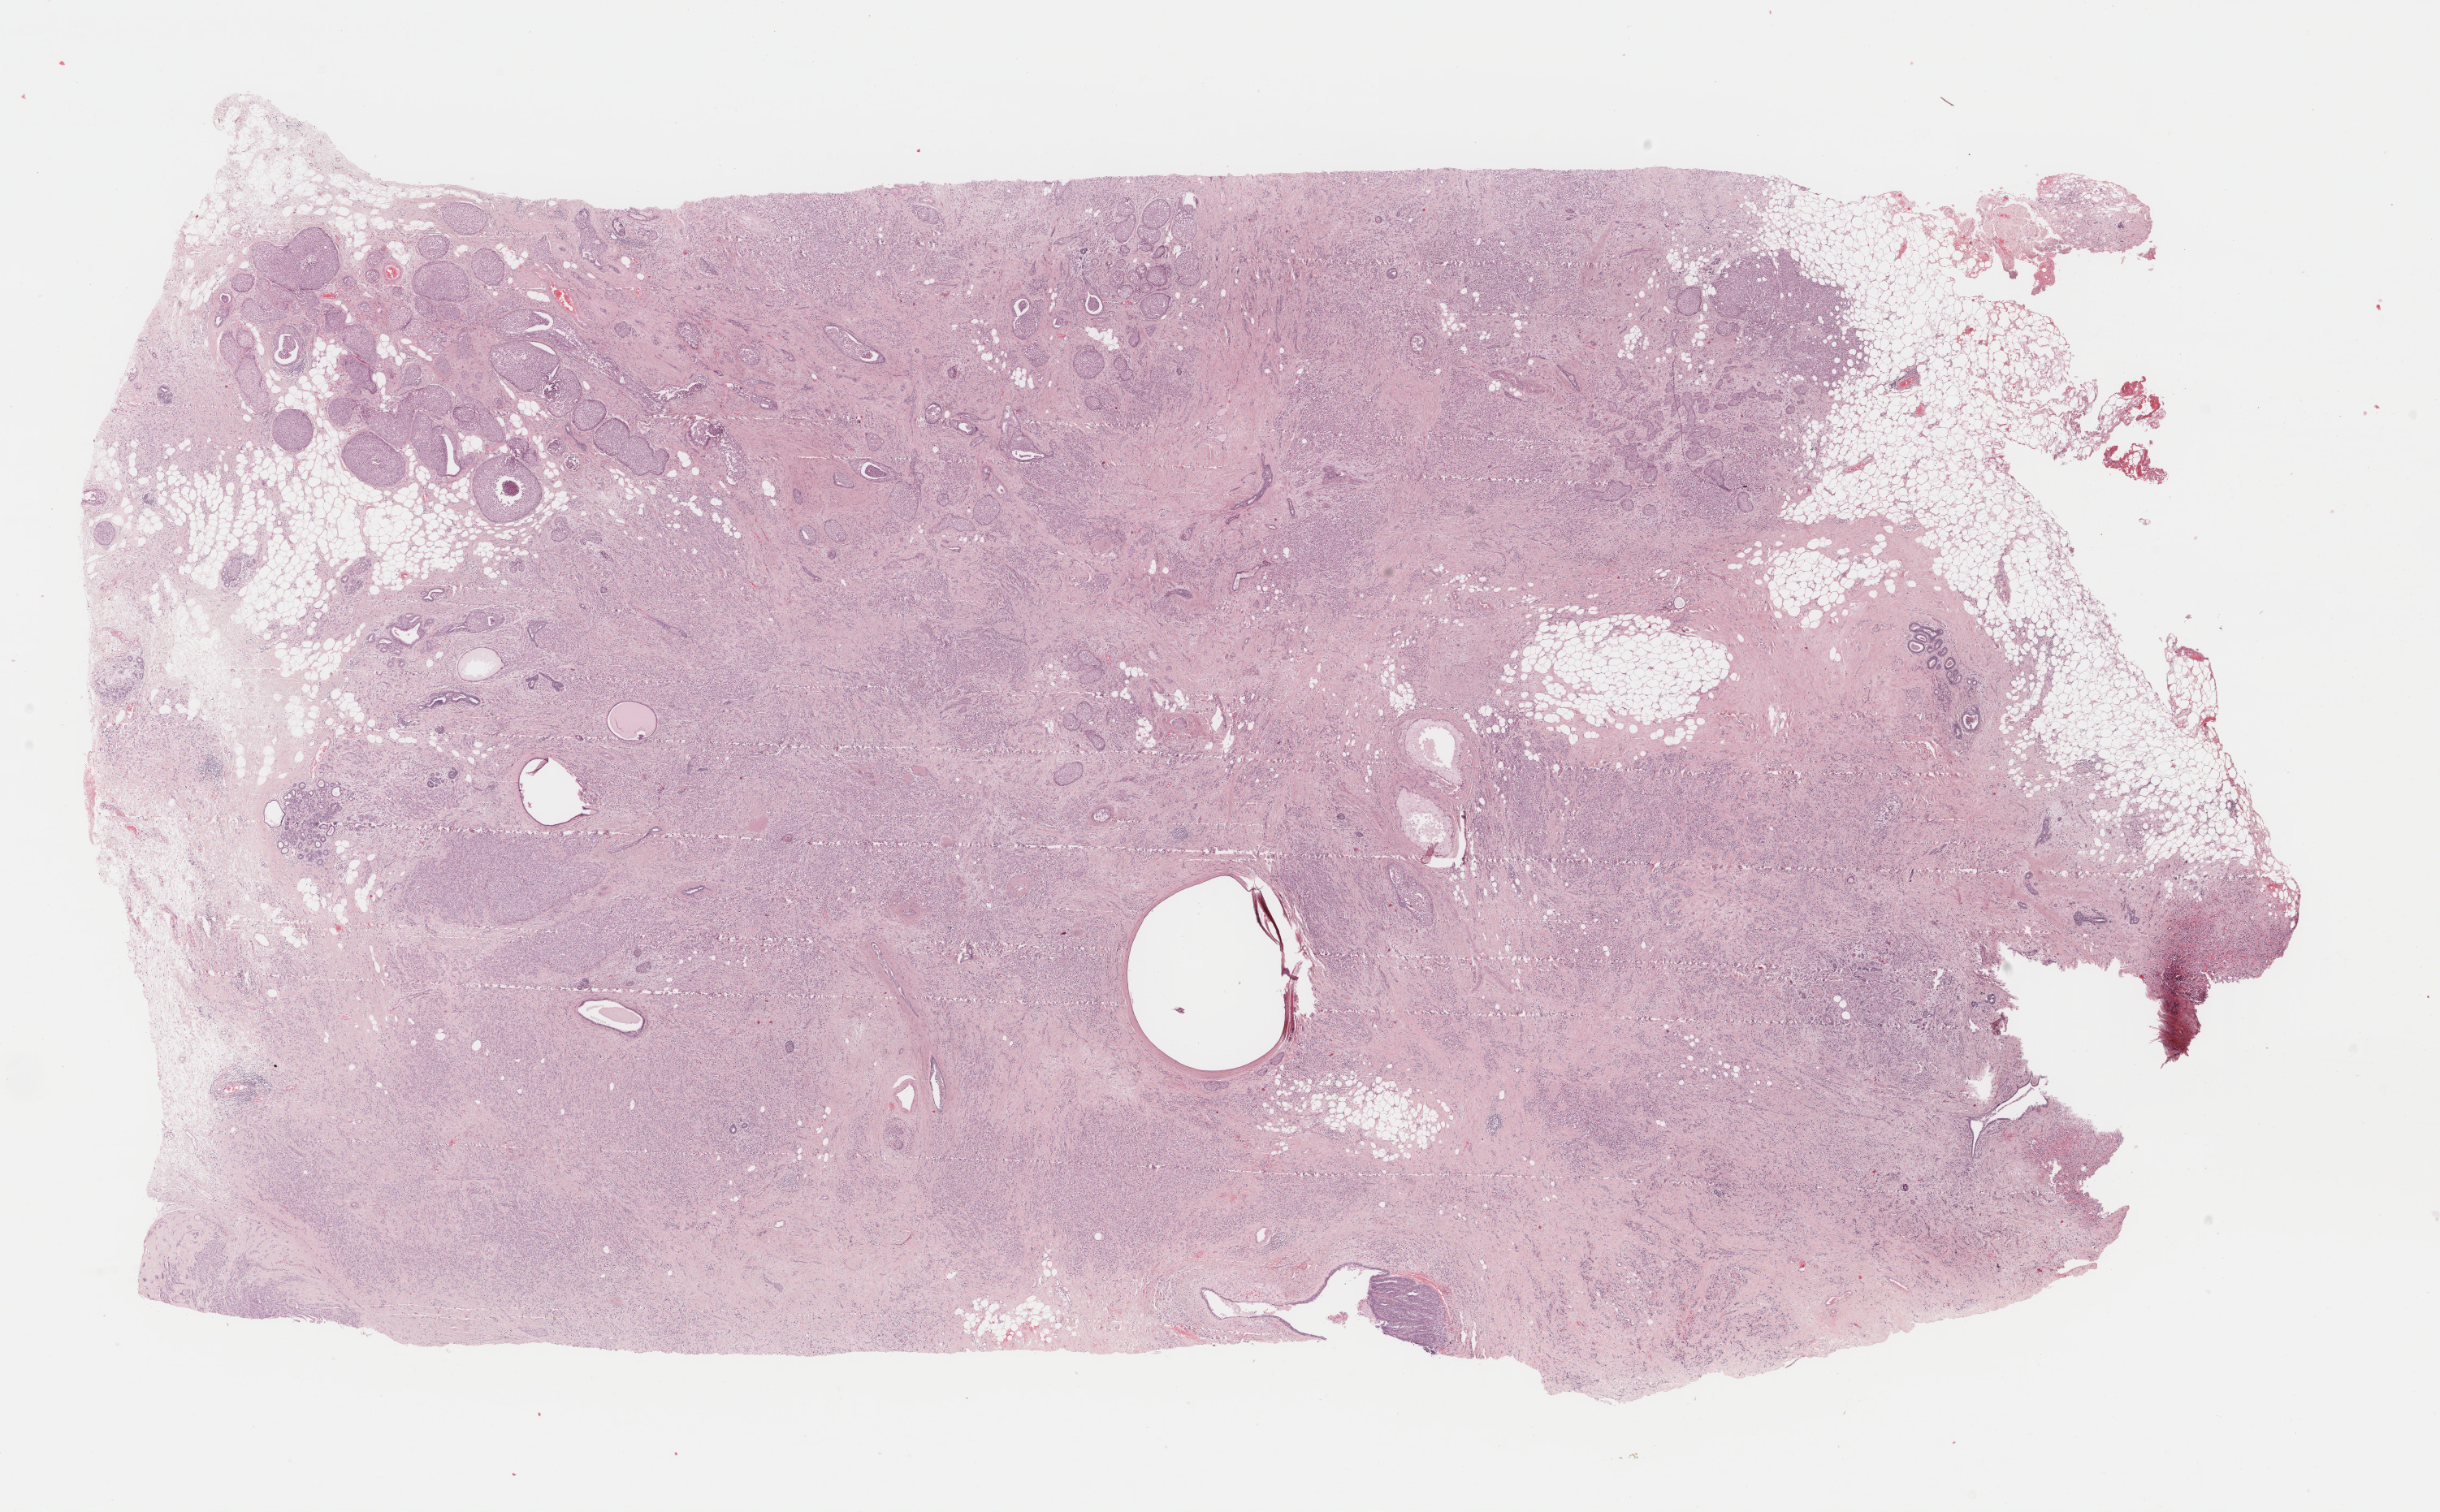
Digitized Hematoxylin and eosin (H&E) stained tissue section (whole slide) — low-resolution overview of the scanned area, about 23.8 x 14.8 mm. FFPE section. Primary tumour sample from the breast. Female, age 56 years at initial diagnosis.
AJCC pathologic stage: IIIC (7th edition). Diagnosis: Lobular carcinoma, NOS. TNM: T3 N3a M0.